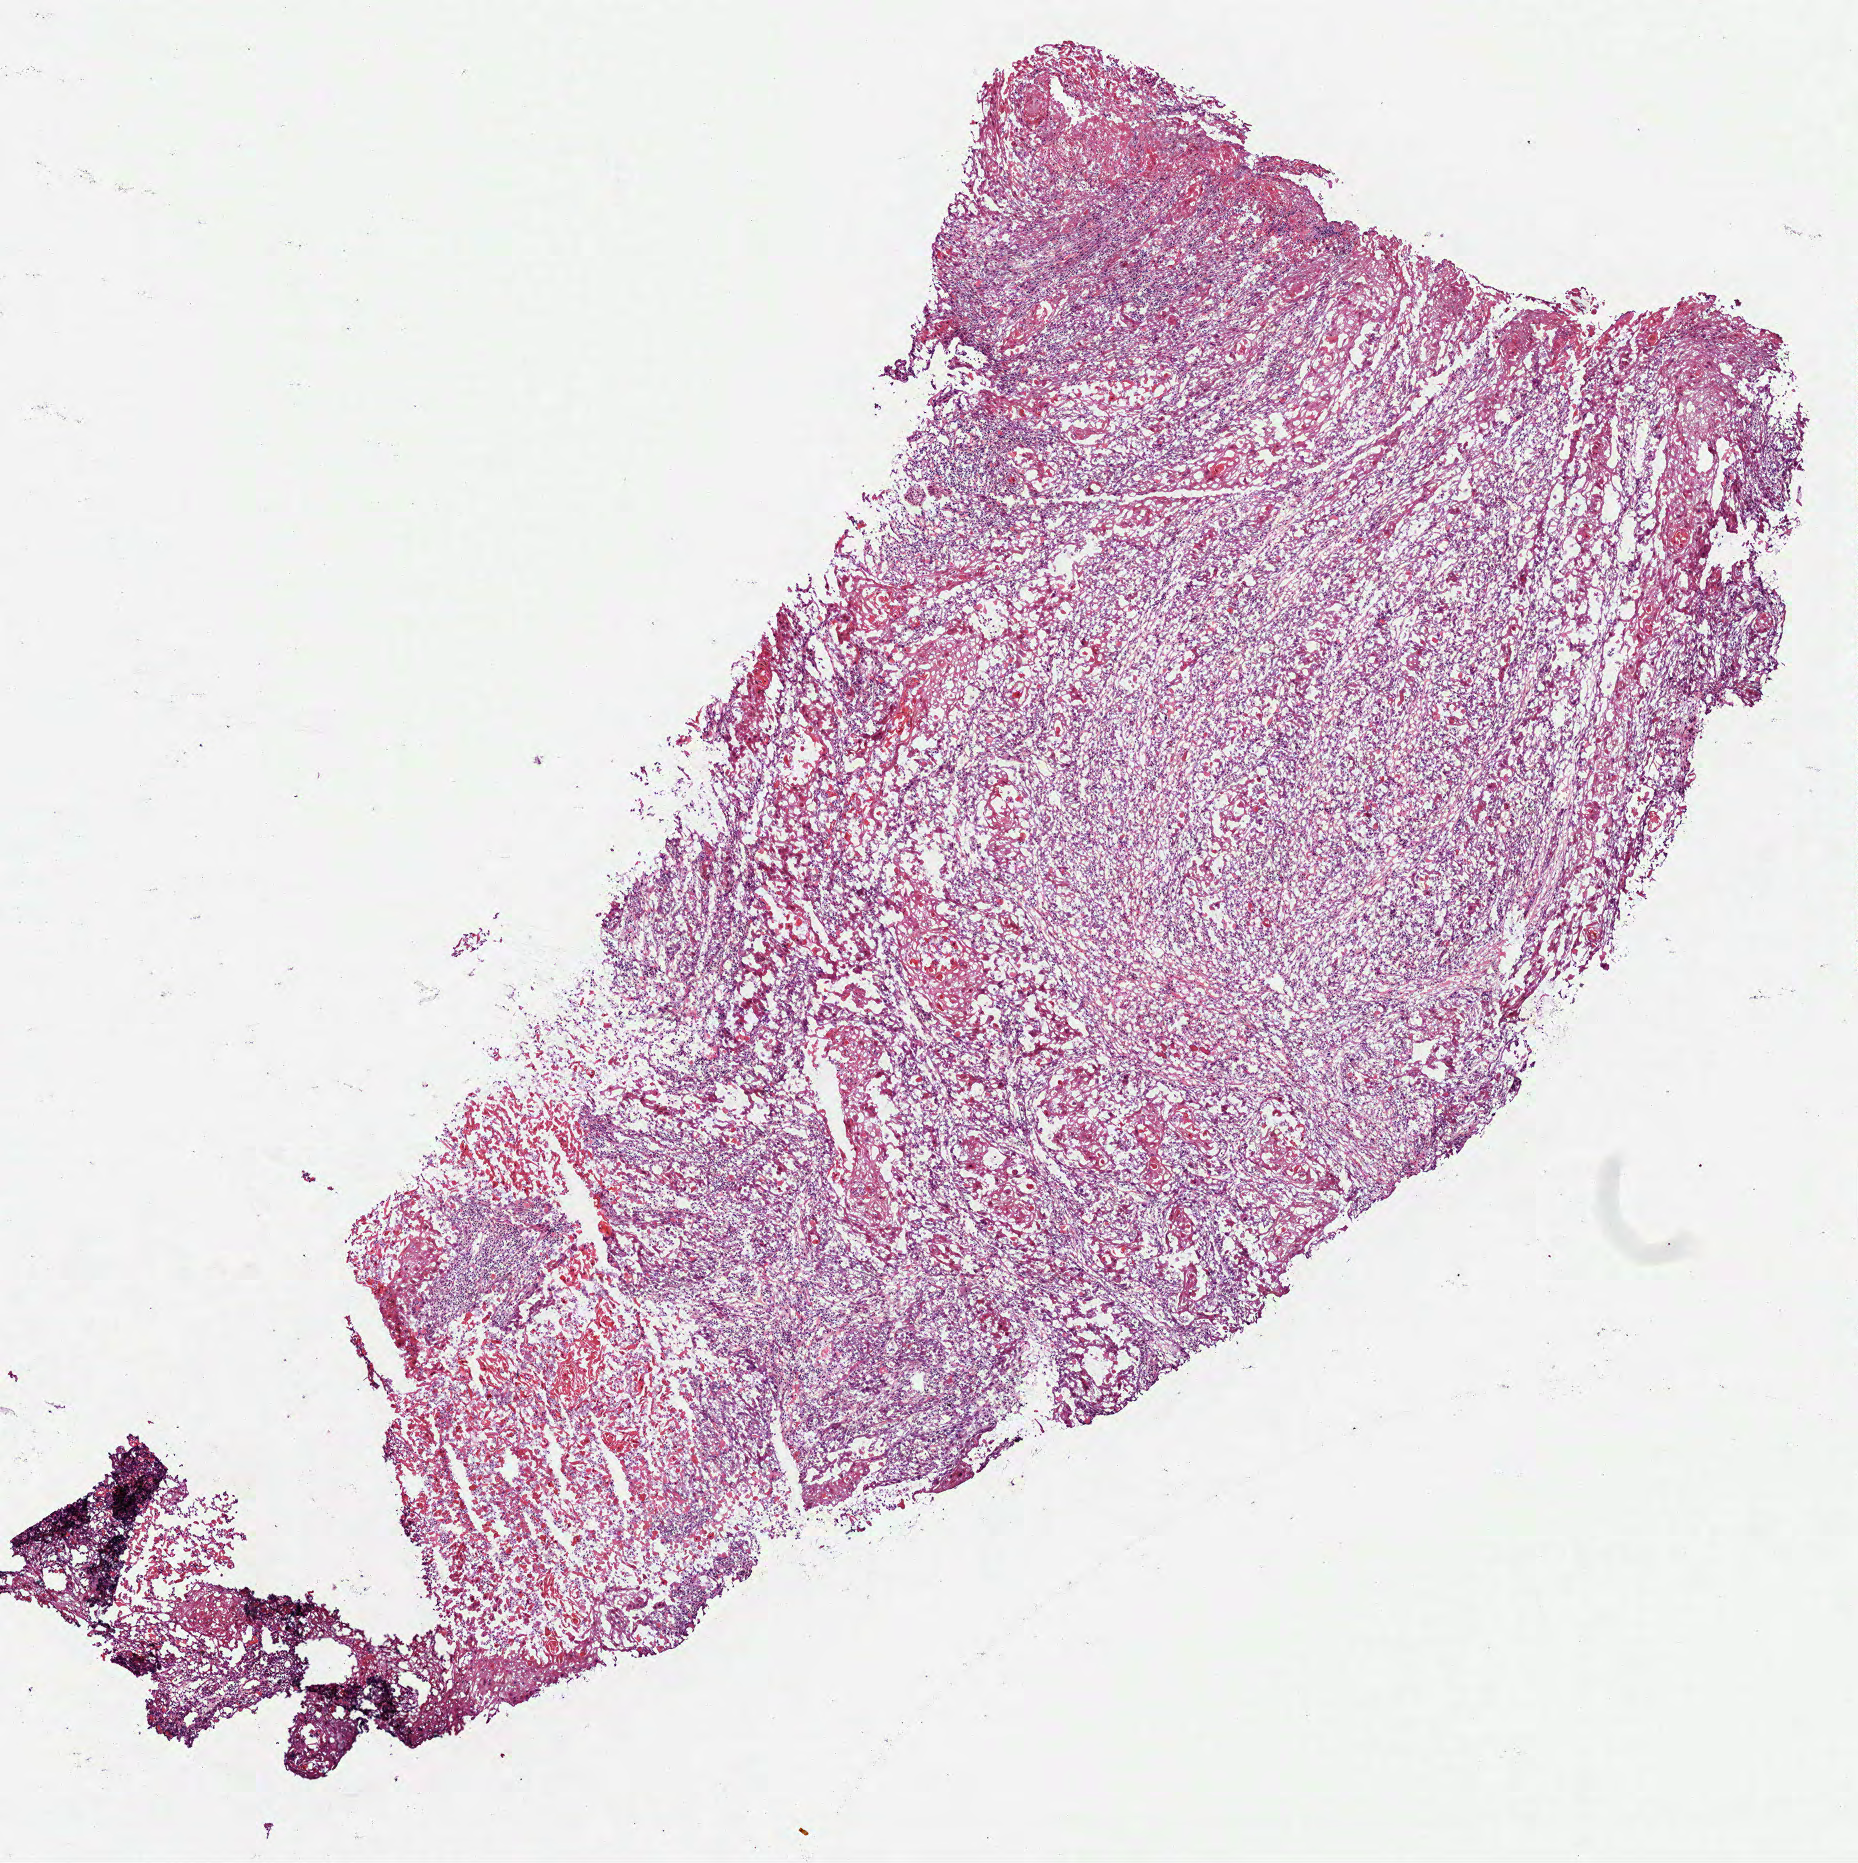
Digitized Hematoxylin and eosin (H&E) stained tissue section (whole slide) — low-resolution overview of the scanned area, about 7.5 x 7.5 mm; frozen section; head and neck, primary tumour sample. Female patient; age at initial diagnosis 83 years. Histologic grade: G2 (moderately differentiated). Composition of this section per pathologist review: tumour cells 90%, tumour nuclei 60%, normal cells 1%, stromal cells 9%, necrosis 0%. Inflammatory infiltration, as recorded: lymphocyte infiltration 30%.
• lymph nodes positive (case pathology): 1 of 30 examined
• histologic diagnosis: Squamous cell carcinoma, NOS (mouth, NOS)
• AJCC pathologic stage: III (6th edition)
• laterality: left